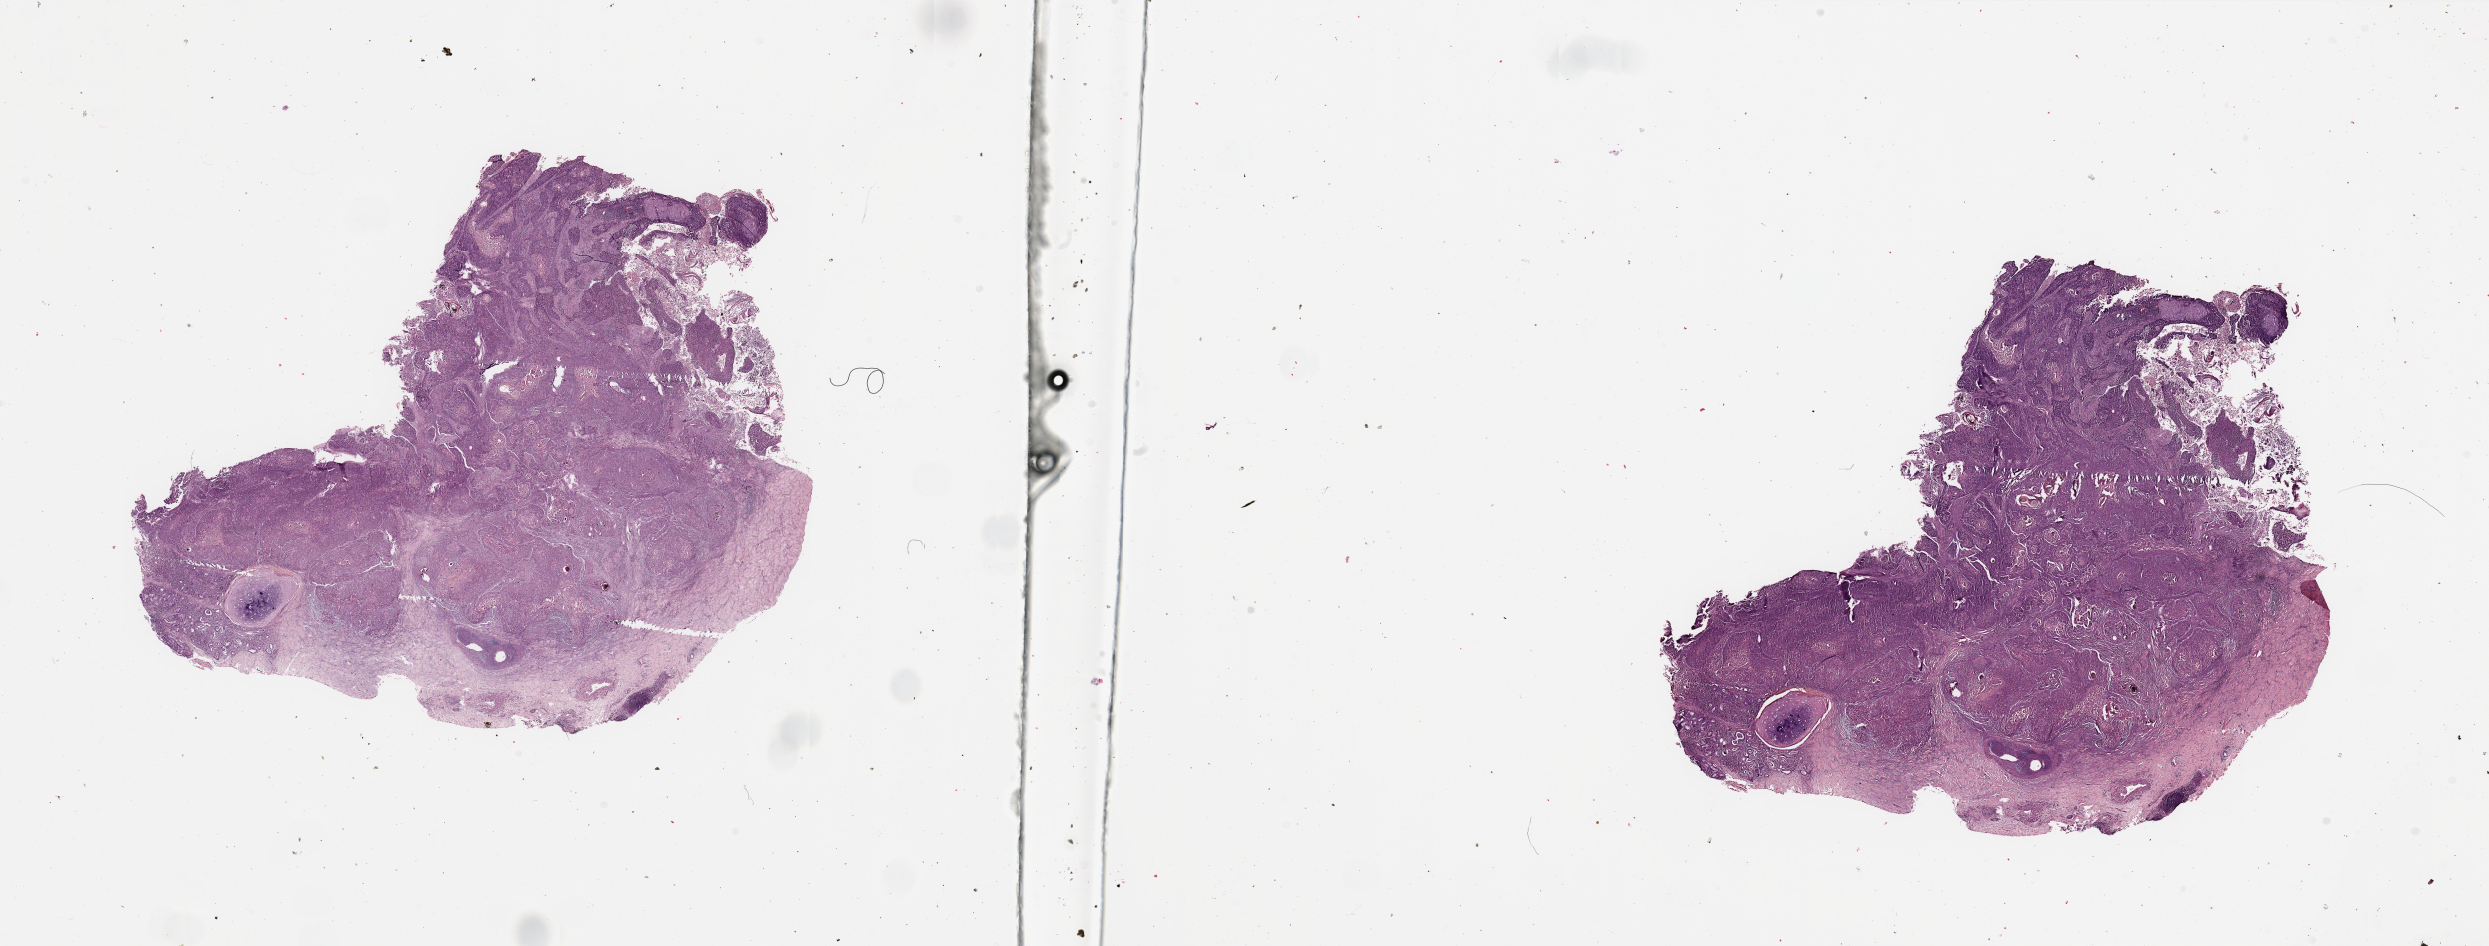
Whole-slide histology image, H&E-stained, whole scanned area (about 39.4 x 15.0 mm) shown as a low-resolution overview; lung, tumour tissue. Male, 46 y/o. Histologic grade: G2 (moderately differentiated).
Primary tumour site (as recorded): left upper lobe. Histologic diagnosis: Squamous cell carcinoma, NOS. AJCC pathologic stage: IIA.